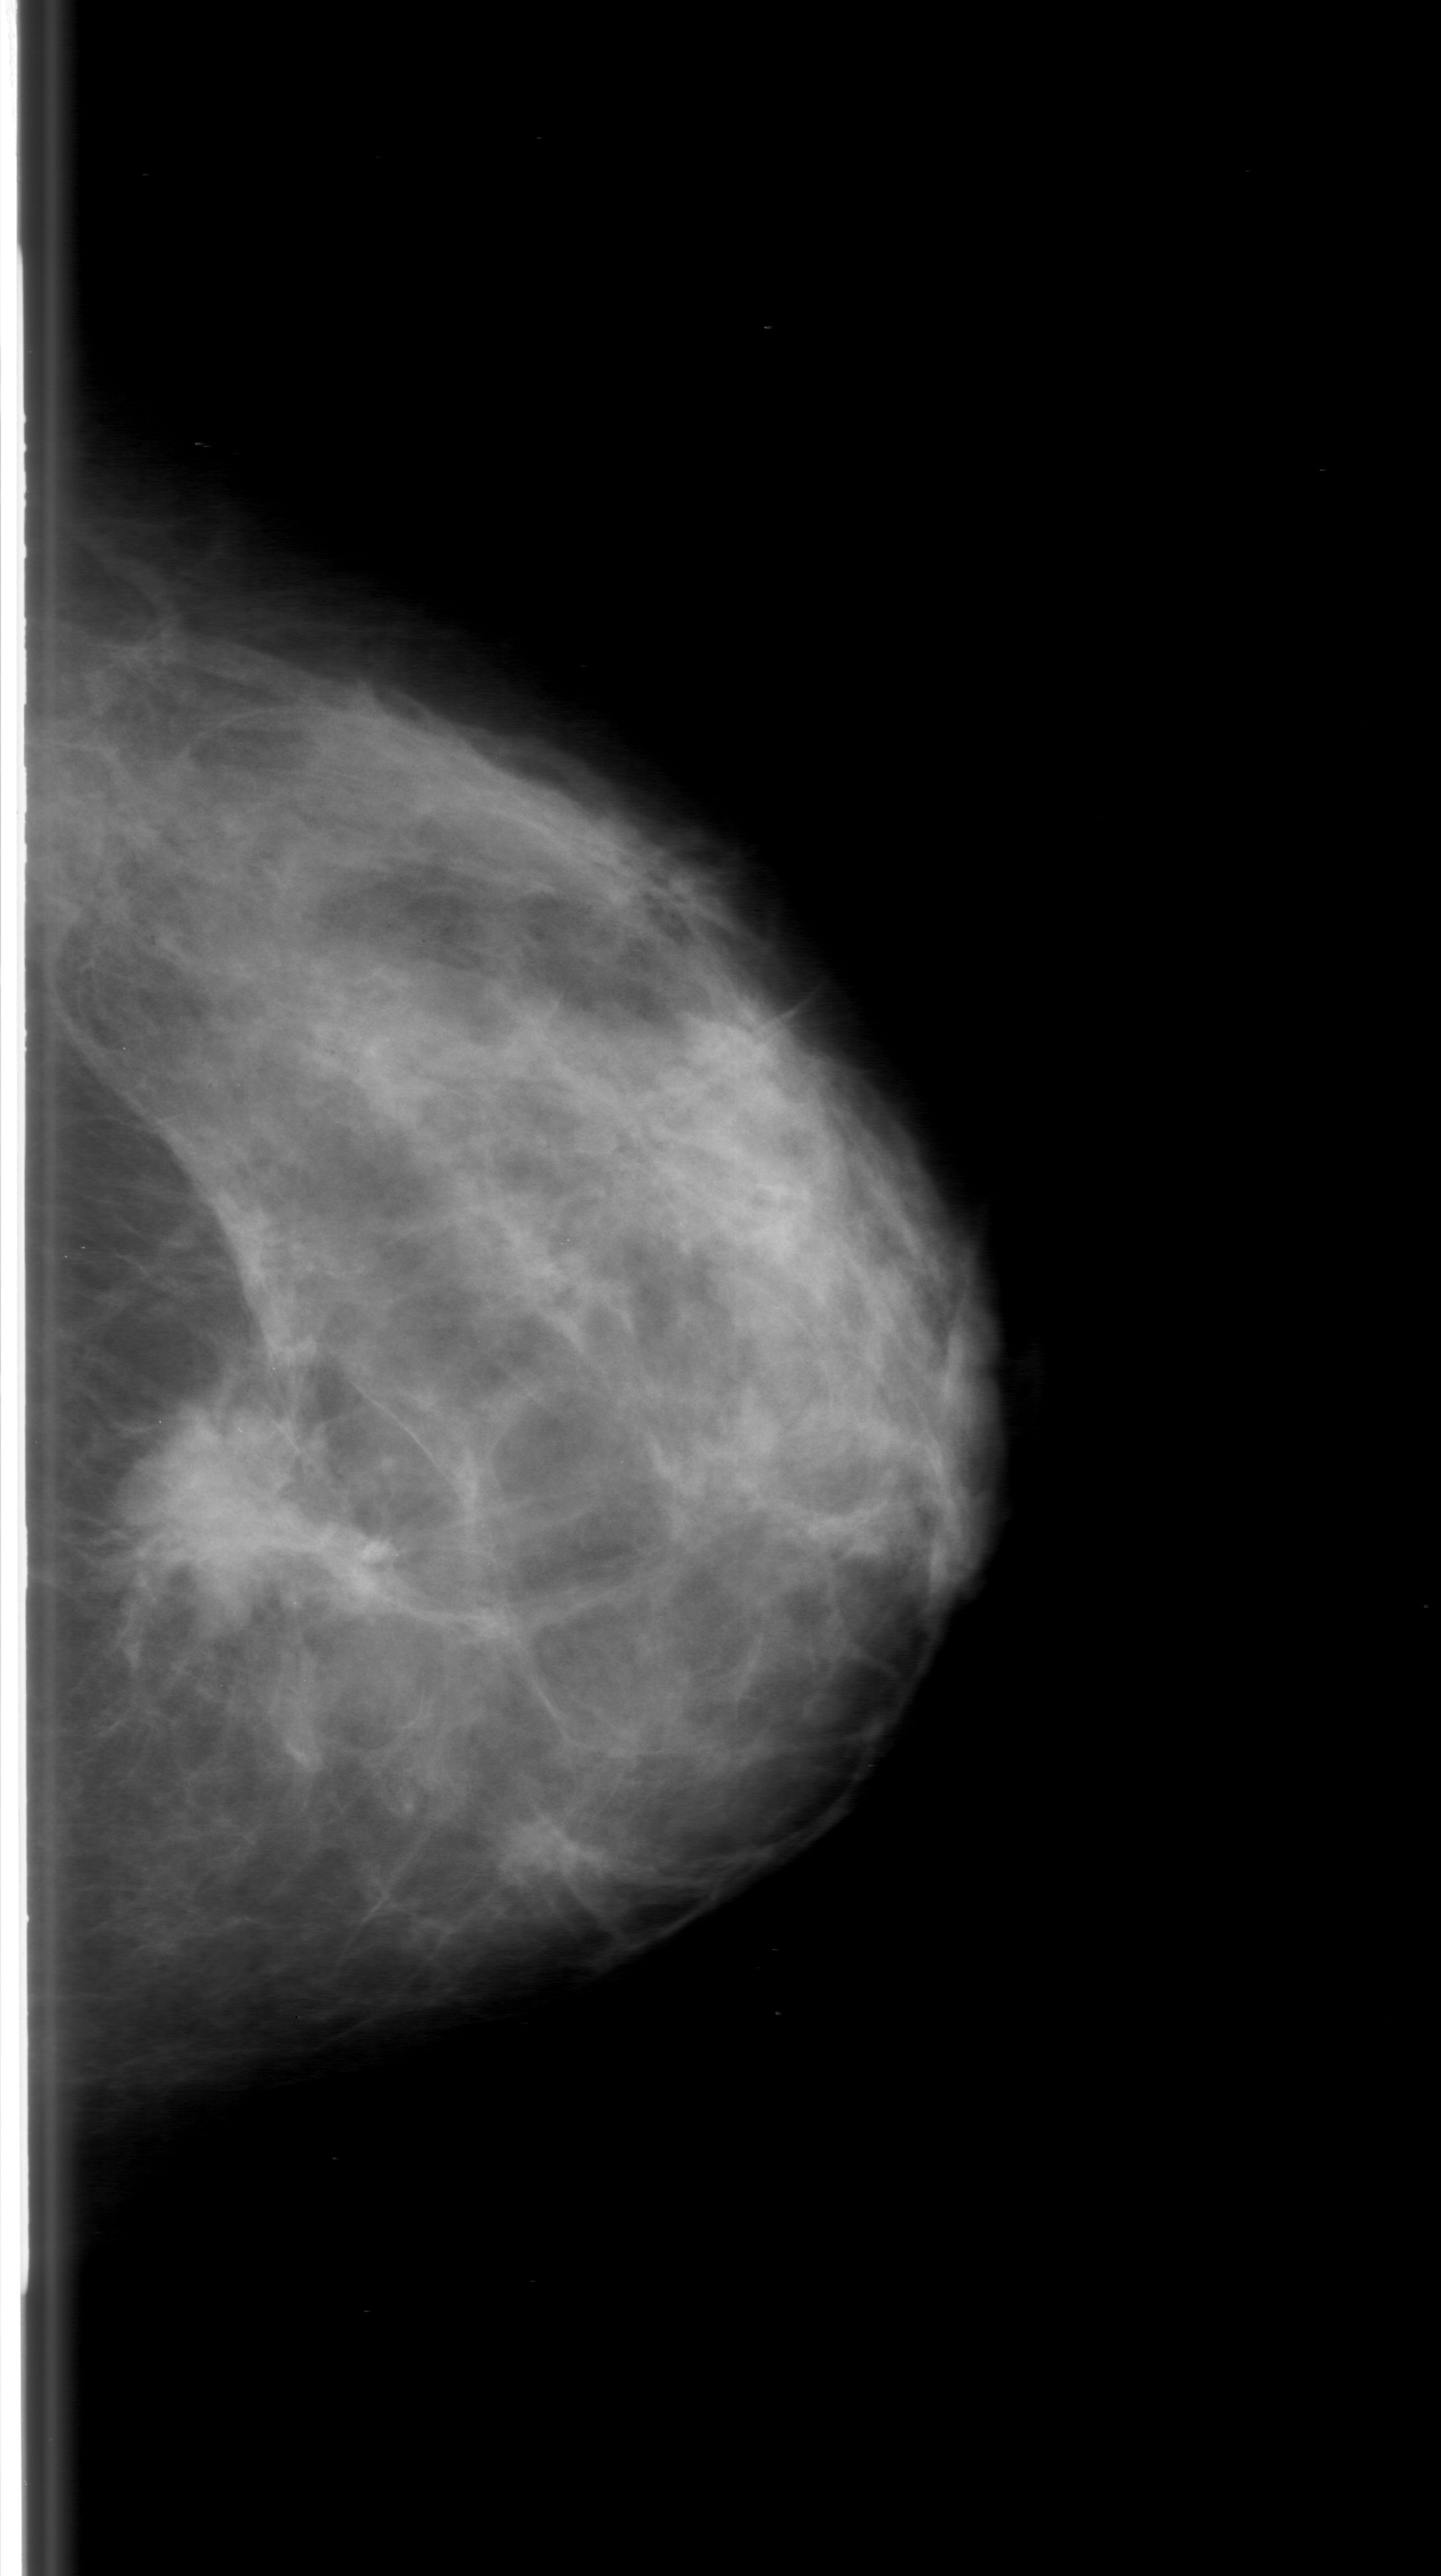
Mammogram (digitized film); left breast; craniocaudal (CC) view; breast composition: heterogeneously dense (BI-RADS density category 3 of 4).
Mass, shape irregular, margins spiculated; BI-RADS assessment category 5; subtlety rating 4 on a 1 (subtle) to 5 (obvious) scale; pathology (as recorded): malignant.